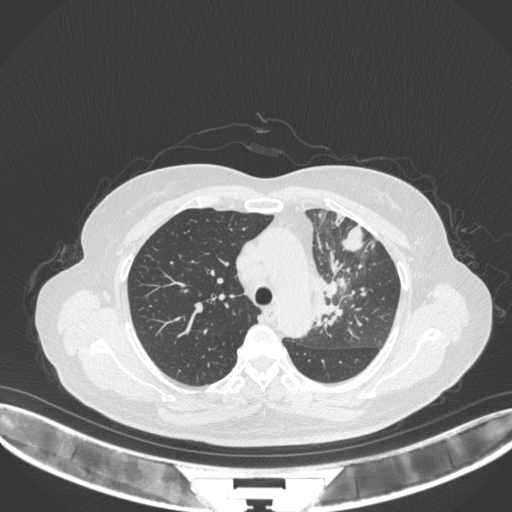
Chest CT, one axial slice. Position 244 of 382 along the scan axis. Reconstruction kernel B31f. Lung window (W 1500 / L -600 HU). 1 mm slice thickness. 512 × 512 image matrix, field of view 400 × 400 mm. Patient: female, 64 years. Case-level facts recorded for this patient, not image findings: clinical TNM (as recorded): T2a N2 M0.
Structures marked on this image (bounding box drawn by a radiologist):
- lung tumour (recorded histology: adenocarcinoma): bounding box [x1, y1, x2, y2] px = [315, 257, 352, 333]
- lung tumour (recorded histology: adenocarcinoma): [336, 226, 366, 257]